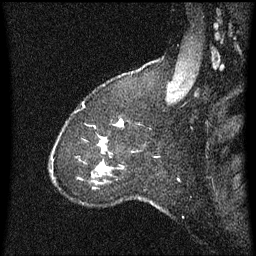
Breast MRI (dynamic contrast-enhanced), one sagittal slice. Position 49 of 60 along the scan axis. Dynamic contrast-enhanced series, image 2 of 3 at this slice position (ordered by acquisition). 1.5 T. TE 4.2 ms, TR 8.4 ms. 256 × 256 image matrix, field of view 200 × 200 mm. Patient: female, 37 years. Case-level facts recorded for this patient, not image findings: setting: breast cancer imaged before/during neoadjuvant chemotherapy; receptor status: HR-positive, HER2-negative.
Outlined on this slice (semi-automatic segmentation, software-assisted and operator-edited):
- analysis volume of interest (the breast-tissue region the enhancement analysis was run in; not a lesion): bounding box (x1, y1, x2, y2) in pixels: (97, 120, 124, 171)
- tumour enhancement mask (voxels above the 70 % enhancement threshold inside the analysis volume of interest): (120, 122, 123, 125)